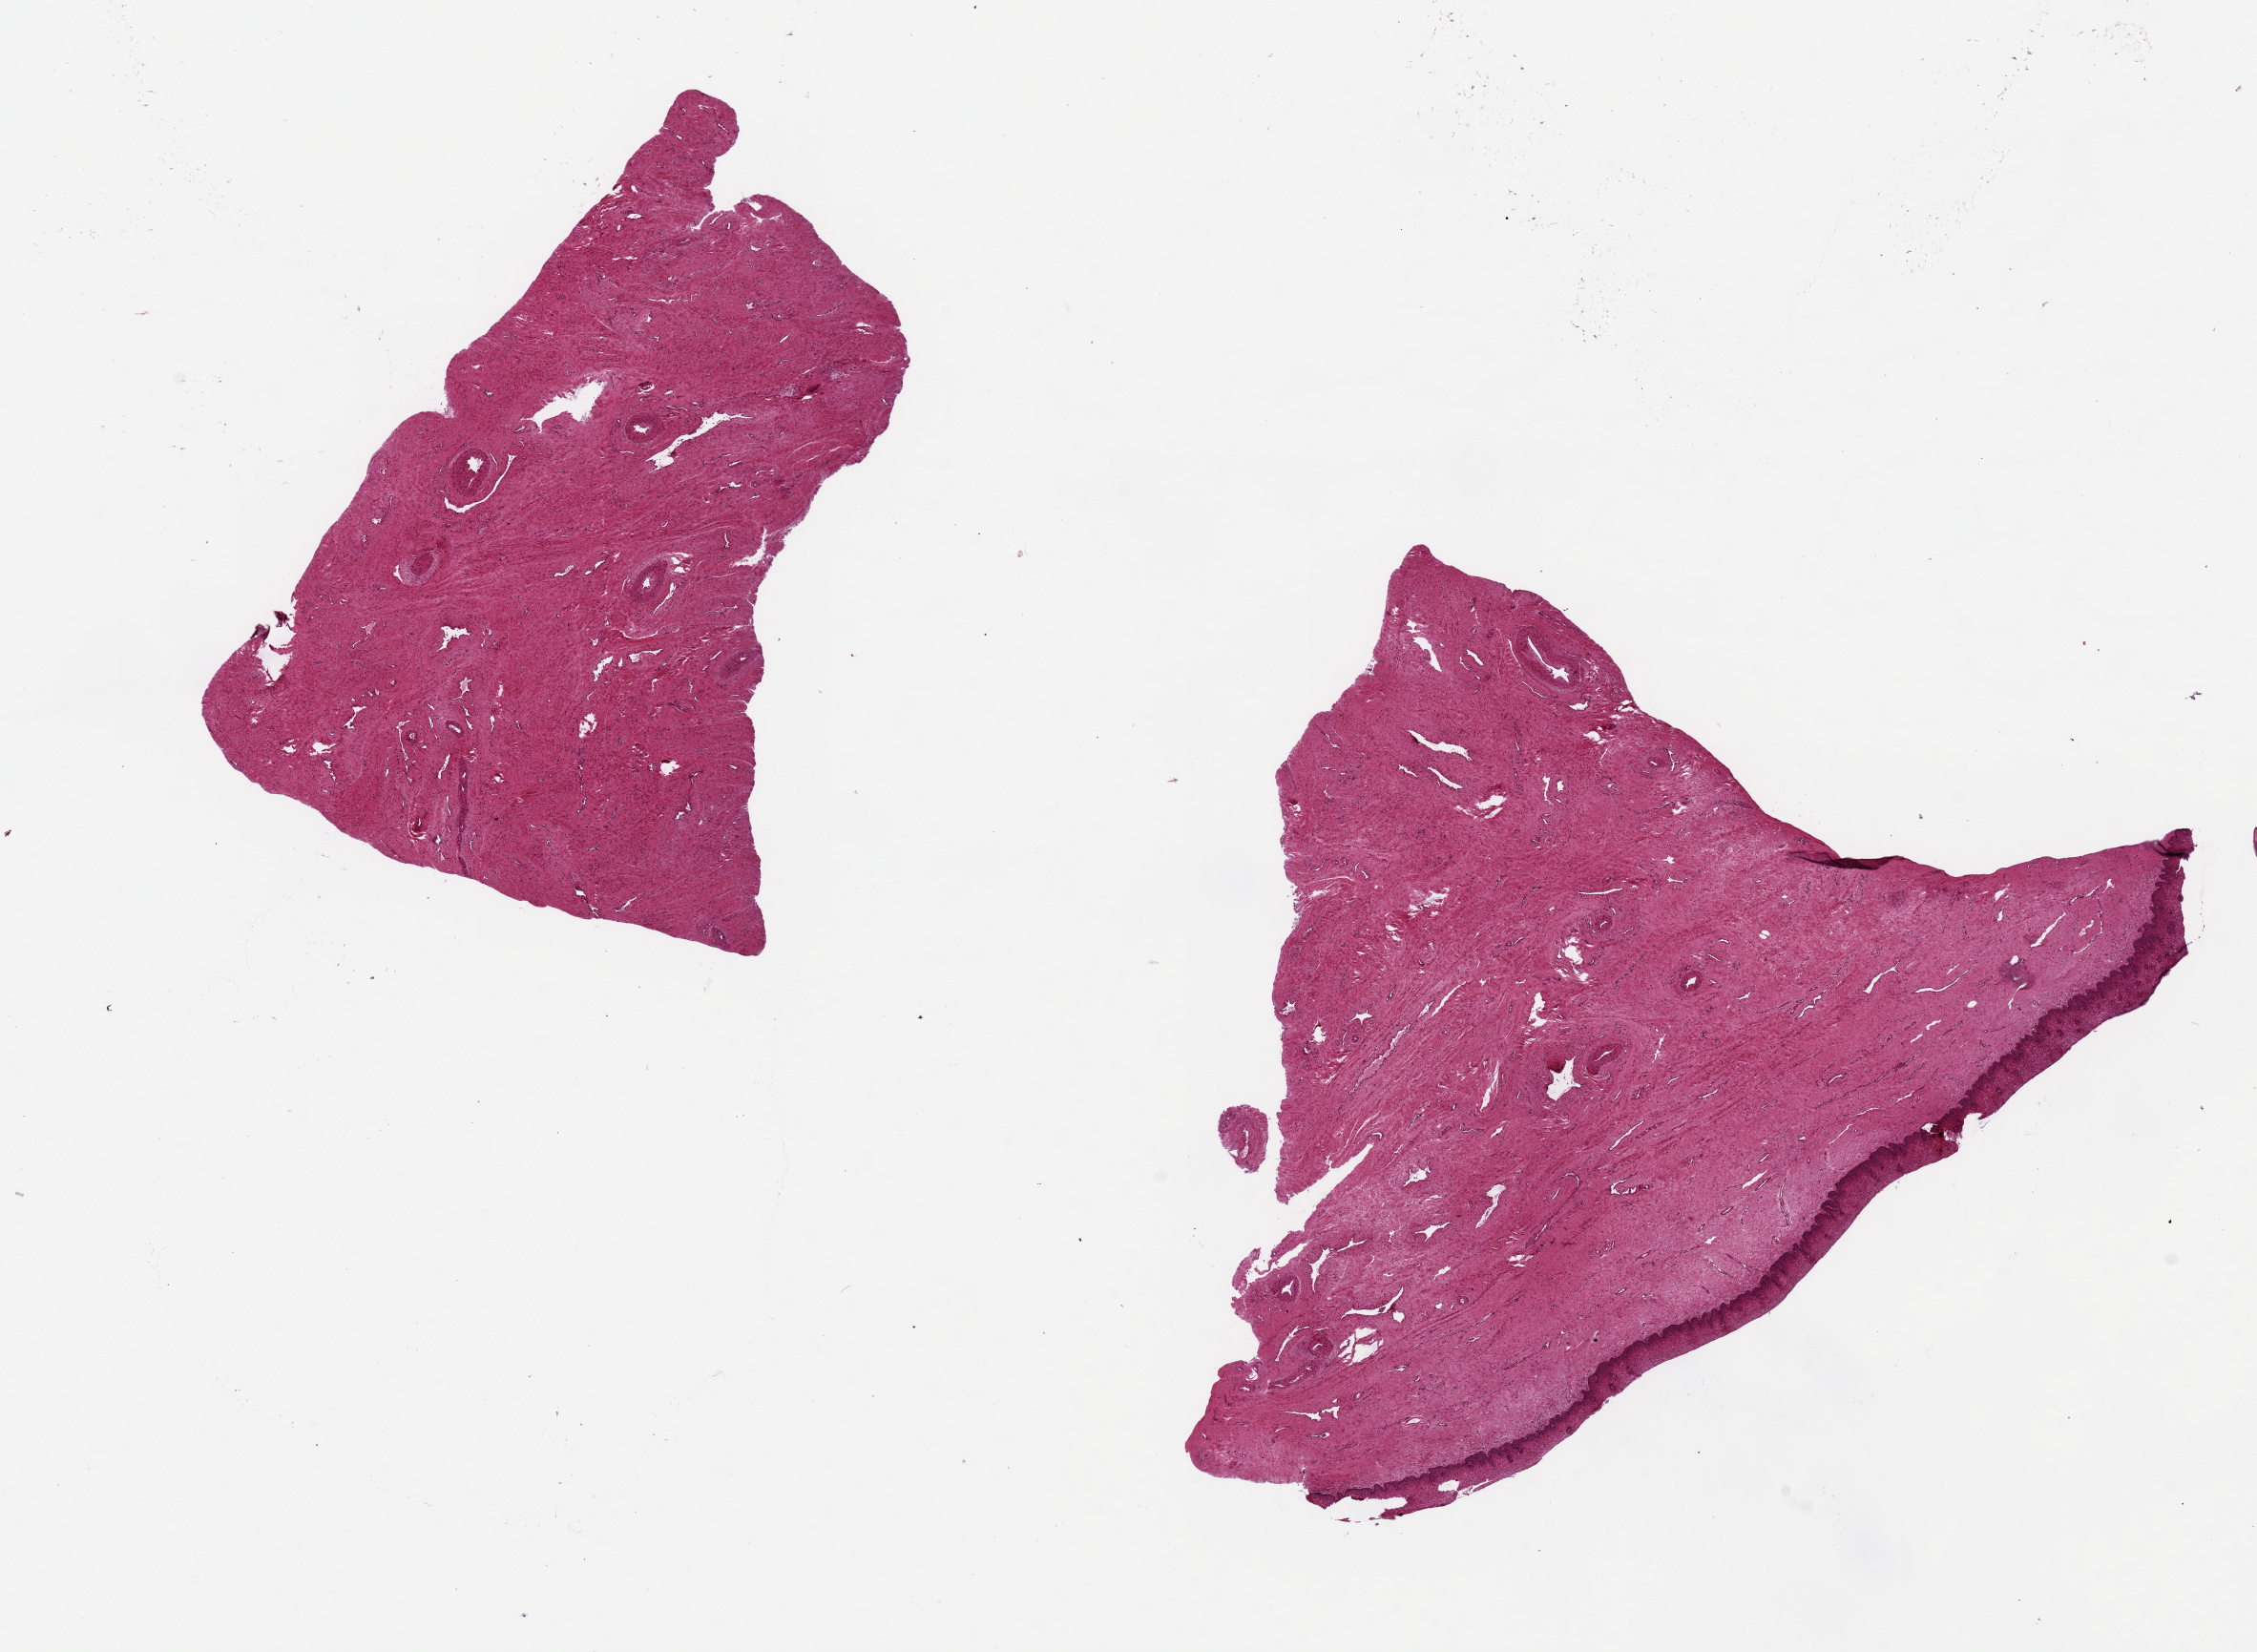
Digitized hematoxylin and eosin (H&E)-stained section, a low-resolution overview of the entire scanned area, about 18.7 x 13.7 mm. PAXgene-fixed paraffin-embedded (PFPE) section. Target tissue: exocervix. Donor tissue sample. Donor: female.
* review note (as recorded): 2 pieces up to 9x6 & 7x5 mm; larger piece is good ectocervix, other has no epithelium; consider as ectocervix